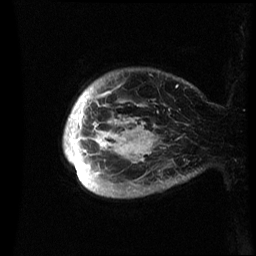
Breast MRI (dynamic contrast-enhanced), one sagittal slice; position 3 of 60 along the scan axis; dynamic contrast-enhanced series, image 2 of 3 at this slice position (ordered by acquisition); 1.5 T; TE 4.2 ms, TR 8.4 ms; 2.4 mm slice thickness; 256 × 256 image matrix, field of view 230 × 230 mm. Female patient, age 48 years.
Outlined on this slice (semi-automatic segmentation, software-assisted and operator-edited):
- analysis volume of interest (the breast-tissue region the enhancement analysis was run in; not a lesion): bounding box <63,70,192,198> (left, top, right, bottom; pixels)
- tumour enhancement mask (voxels above the 70 % enhancement threshold inside the analysis volume of interest): <64,91,153,180>